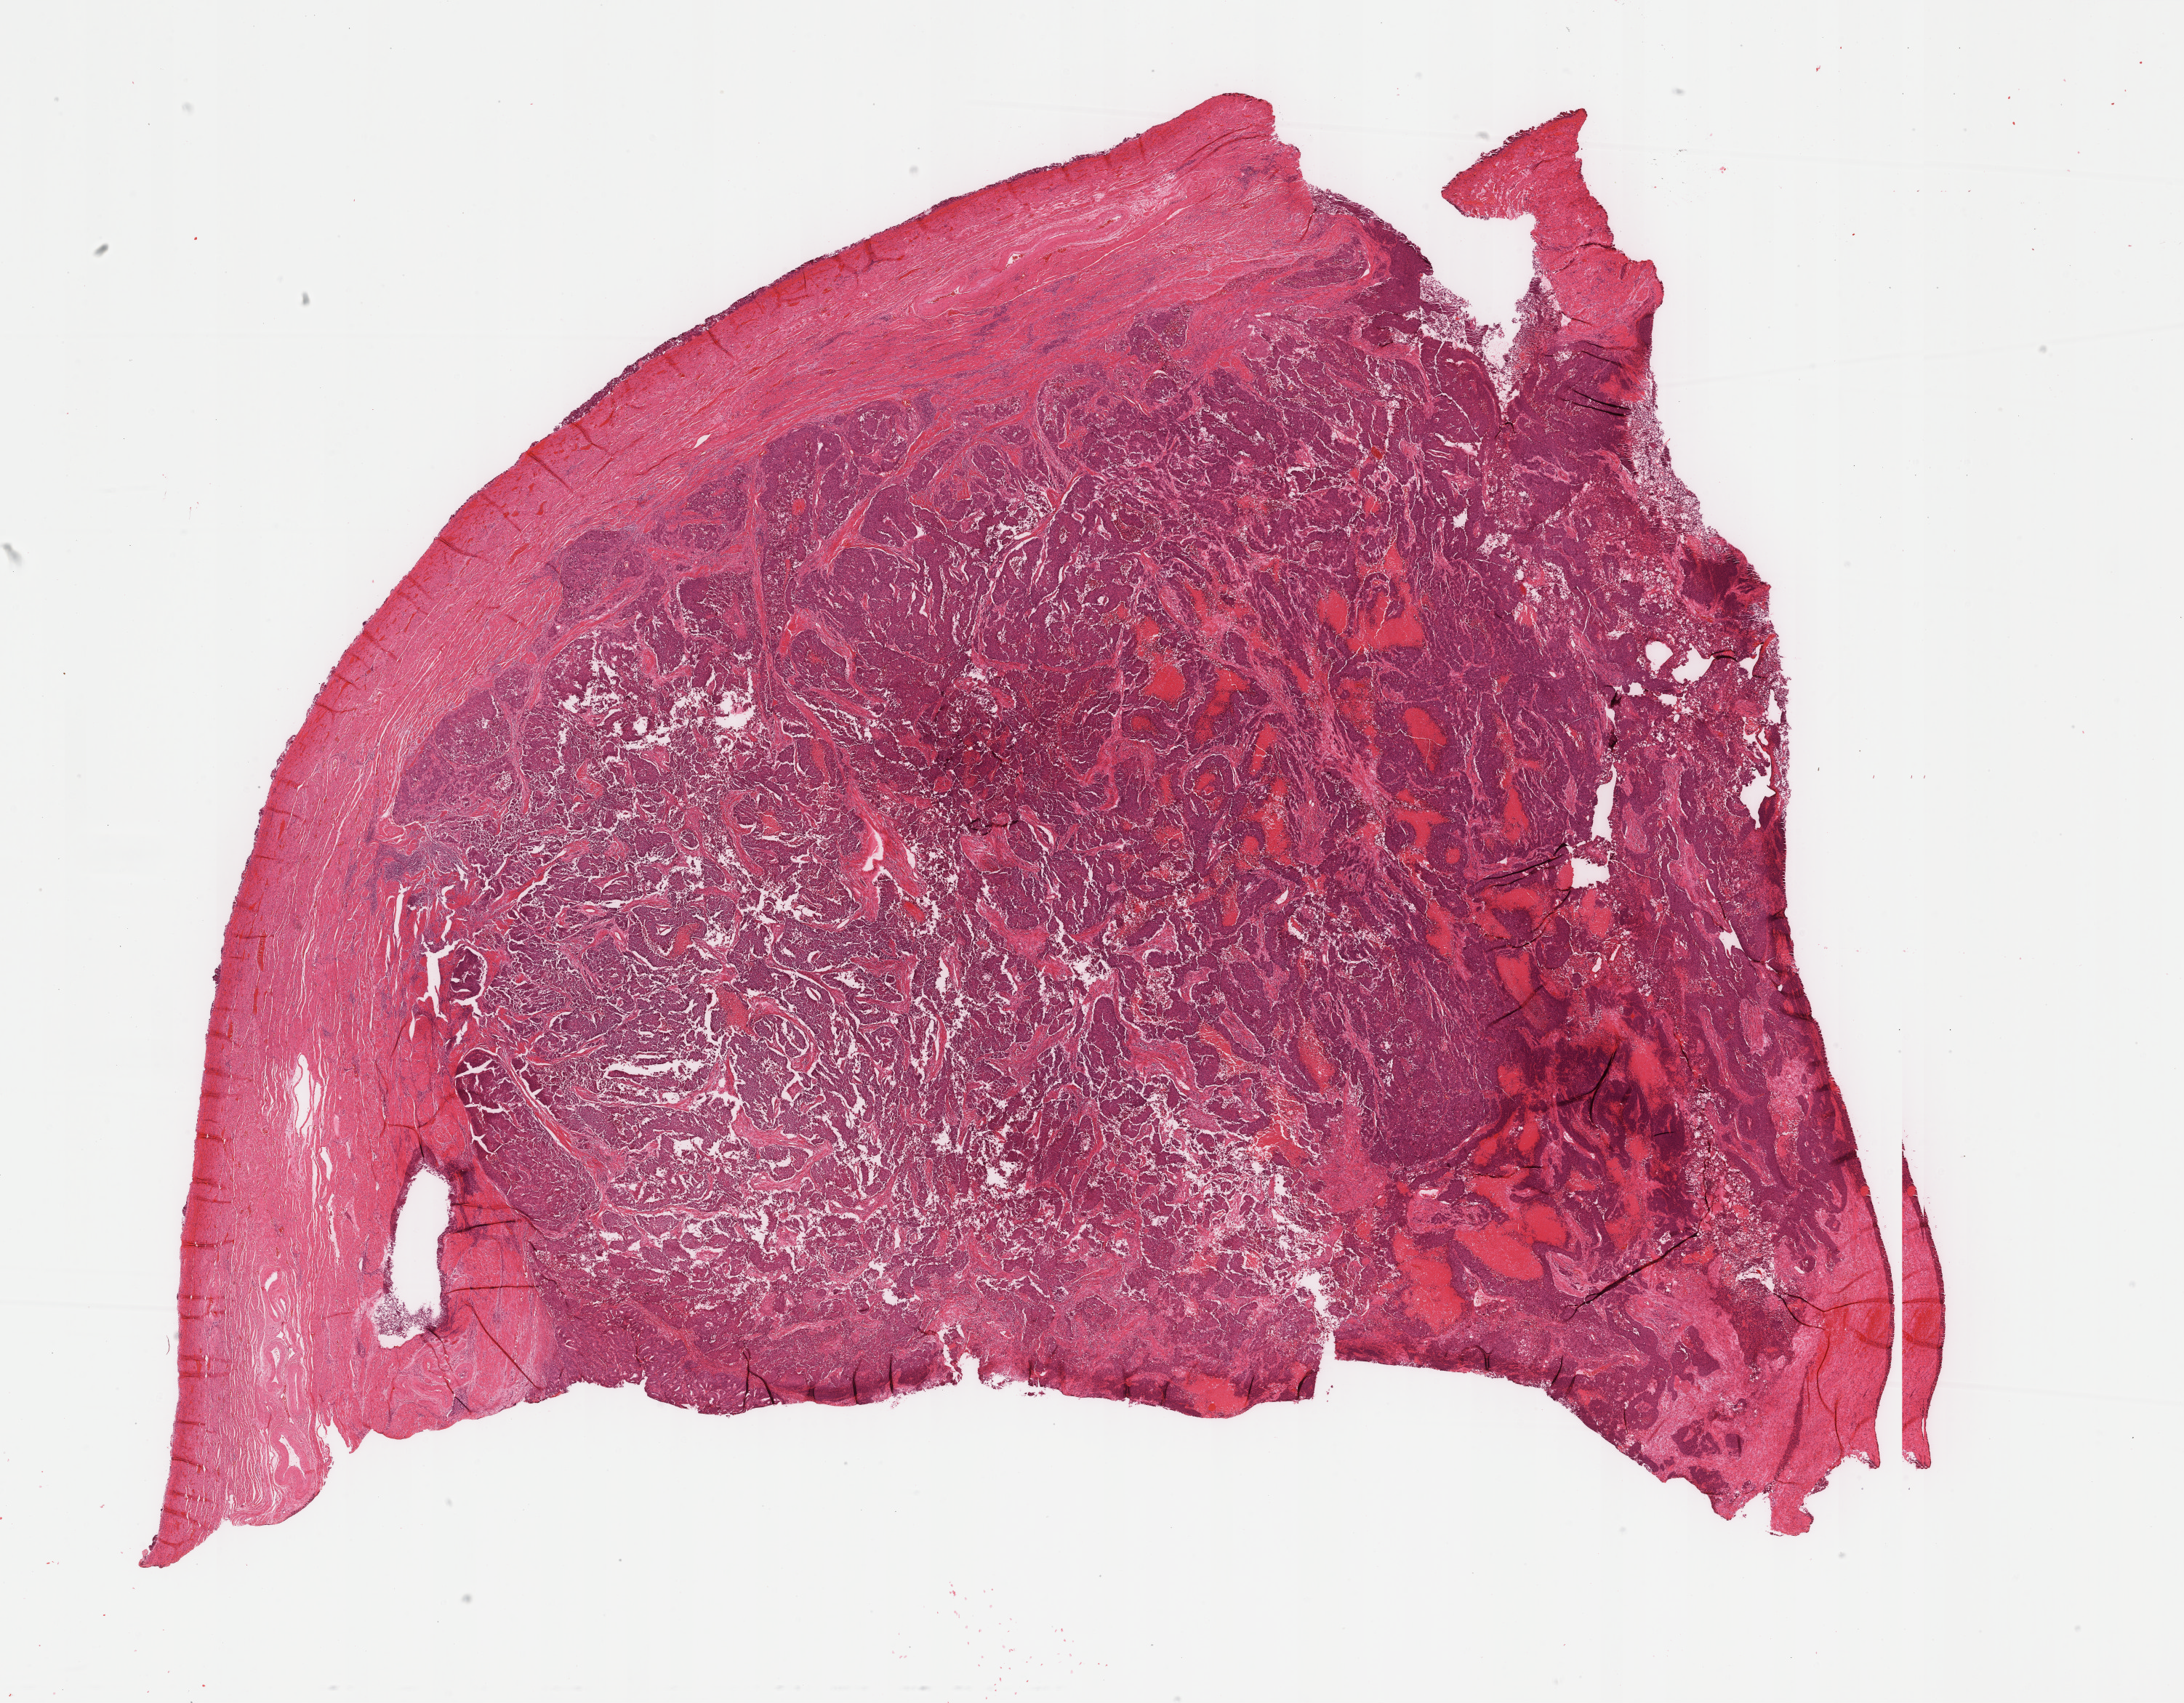
Whole-slide histology image, Hematoxylin and eosin (H&E) stained, a low-resolution overview of the entire scanned area, about 23.8 x 18.6 mm (acquisition: 40x scan), FFPE section, sample: primary tumour, uterus. Patient: female, age at initial diagnosis 63 years. Histologic grade: G3 (poorly differentiated).
Pathologic diagnosis: Endometrioid adenocarcinoma, NOS. FIGO stage: IC.